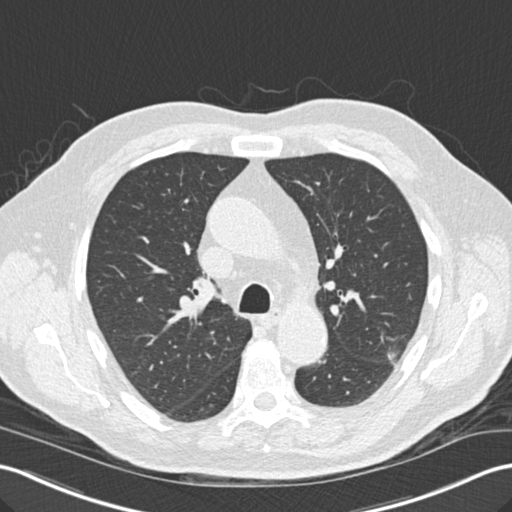
Chest CT (low-dose screening protocol), one axial image. Third screening round (two years after baseline). Lung window (W 1500 / L -600 HU). 2 mm slice thickness. Standard (soft-tissue) reconstruction kernel (B30f). 120 kVp. Slice 57 of 157 in the series. 512 × 512 image matrix, field of view 354 × 354 mm. Male, age 67 years at enrolment. Former smoker at enrolment.
• Lesion marked by an expert reader, bounding box (x1, y1, x2, y2) in pixels: (365, 327, 417, 377).
• The screening reader recorded 2 non-calcified nodules or masses ≥4 mm on this exam (left upper lobe, left lower lobe); which of them this box marks is not recorded.
• Lung cancer was diagnosed 55 days after this screen: squamous cell carcinoma, large cell, nonkeratinizing, NOS, left upper lobe, moderately differentiated (G2), stage IA (AJCC 6th edition), 15 mm at pathology.